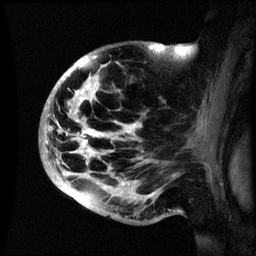
Breast MRI (dynamic contrast-enhanced), one sagittal slice; slice 39 of 60 in the series (ordered by position); dynamic contrast-enhanced series, image 2 of 3 at this slice position (ordered by acquisition); 1.5 T; TE 4.2 ms, TR 8.4 ms; 2.4 mm slice thickness; 256 × 256 image matrix, field of view 230 × 230 mm. Patient: female, 48 years.
Outlined on this slice (semi-automatic segmentation, software-assisted and operator-edited):
- analysis volume of interest (the breast-tissue region the enhancement analysis was run in; not a lesion): box from (x=41, y=43) to (x=195, y=222) px
- tumour enhancement mask (voxels above the 70 % enhancement threshold inside the analysis volume of interest): (x=46, y=43)–(x=156, y=194)